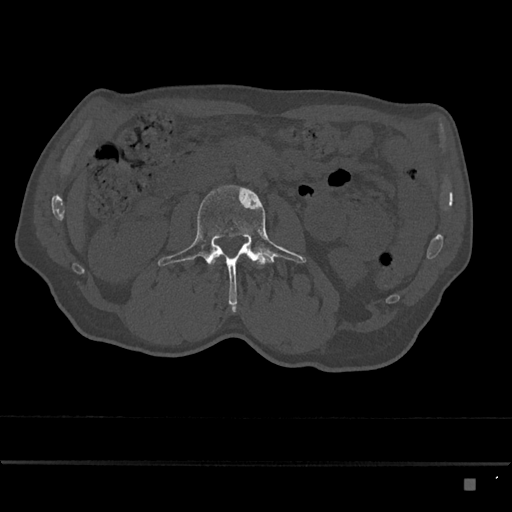
CT including the spine, one axial slice. Position 415 of 797 along the scan axis. 120 kVp. Bone window (W 1800 / L 400 HU). 0.5 mm slice thickness. 512 × 512 image matrix. Patient: male, 72 years. Case-level facts recorded for this patient, not image findings: primary cancer: prostate.
Annotated regions visible in this slice (semi-automatically segmented with operator editing):
- L2 vertebra: bounding box (x1, y1, x2, y2) in pixels: (211, 256, 219, 269)
- L3 vertebra: (158, 185, 306, 312)